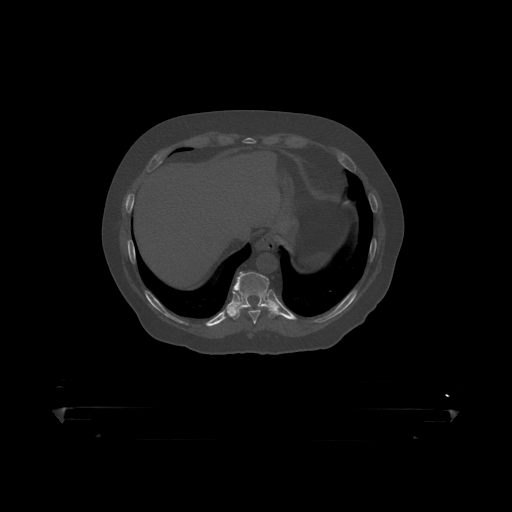
CT including the spine, one axial slice; slice 225 of 390 in the series (ordered by position); 120 kVp; bone window (W 1800 / L 400 HU); 1.25 mm slice thickness; 512 × 512 image matrix, field of view 650 × 650 mm. Patient: male, 60 years. Case-level facts recorded for this patient, not image findings: primary cancer: prostate.
Annotated regions visible in this slice (semi-automatically segmented with operator editing):
- T10 vertebra: bounding box <235,272,278,317> (left, top, right, bottom; pixels)
- T9 vertebra: <233,279,266,319>